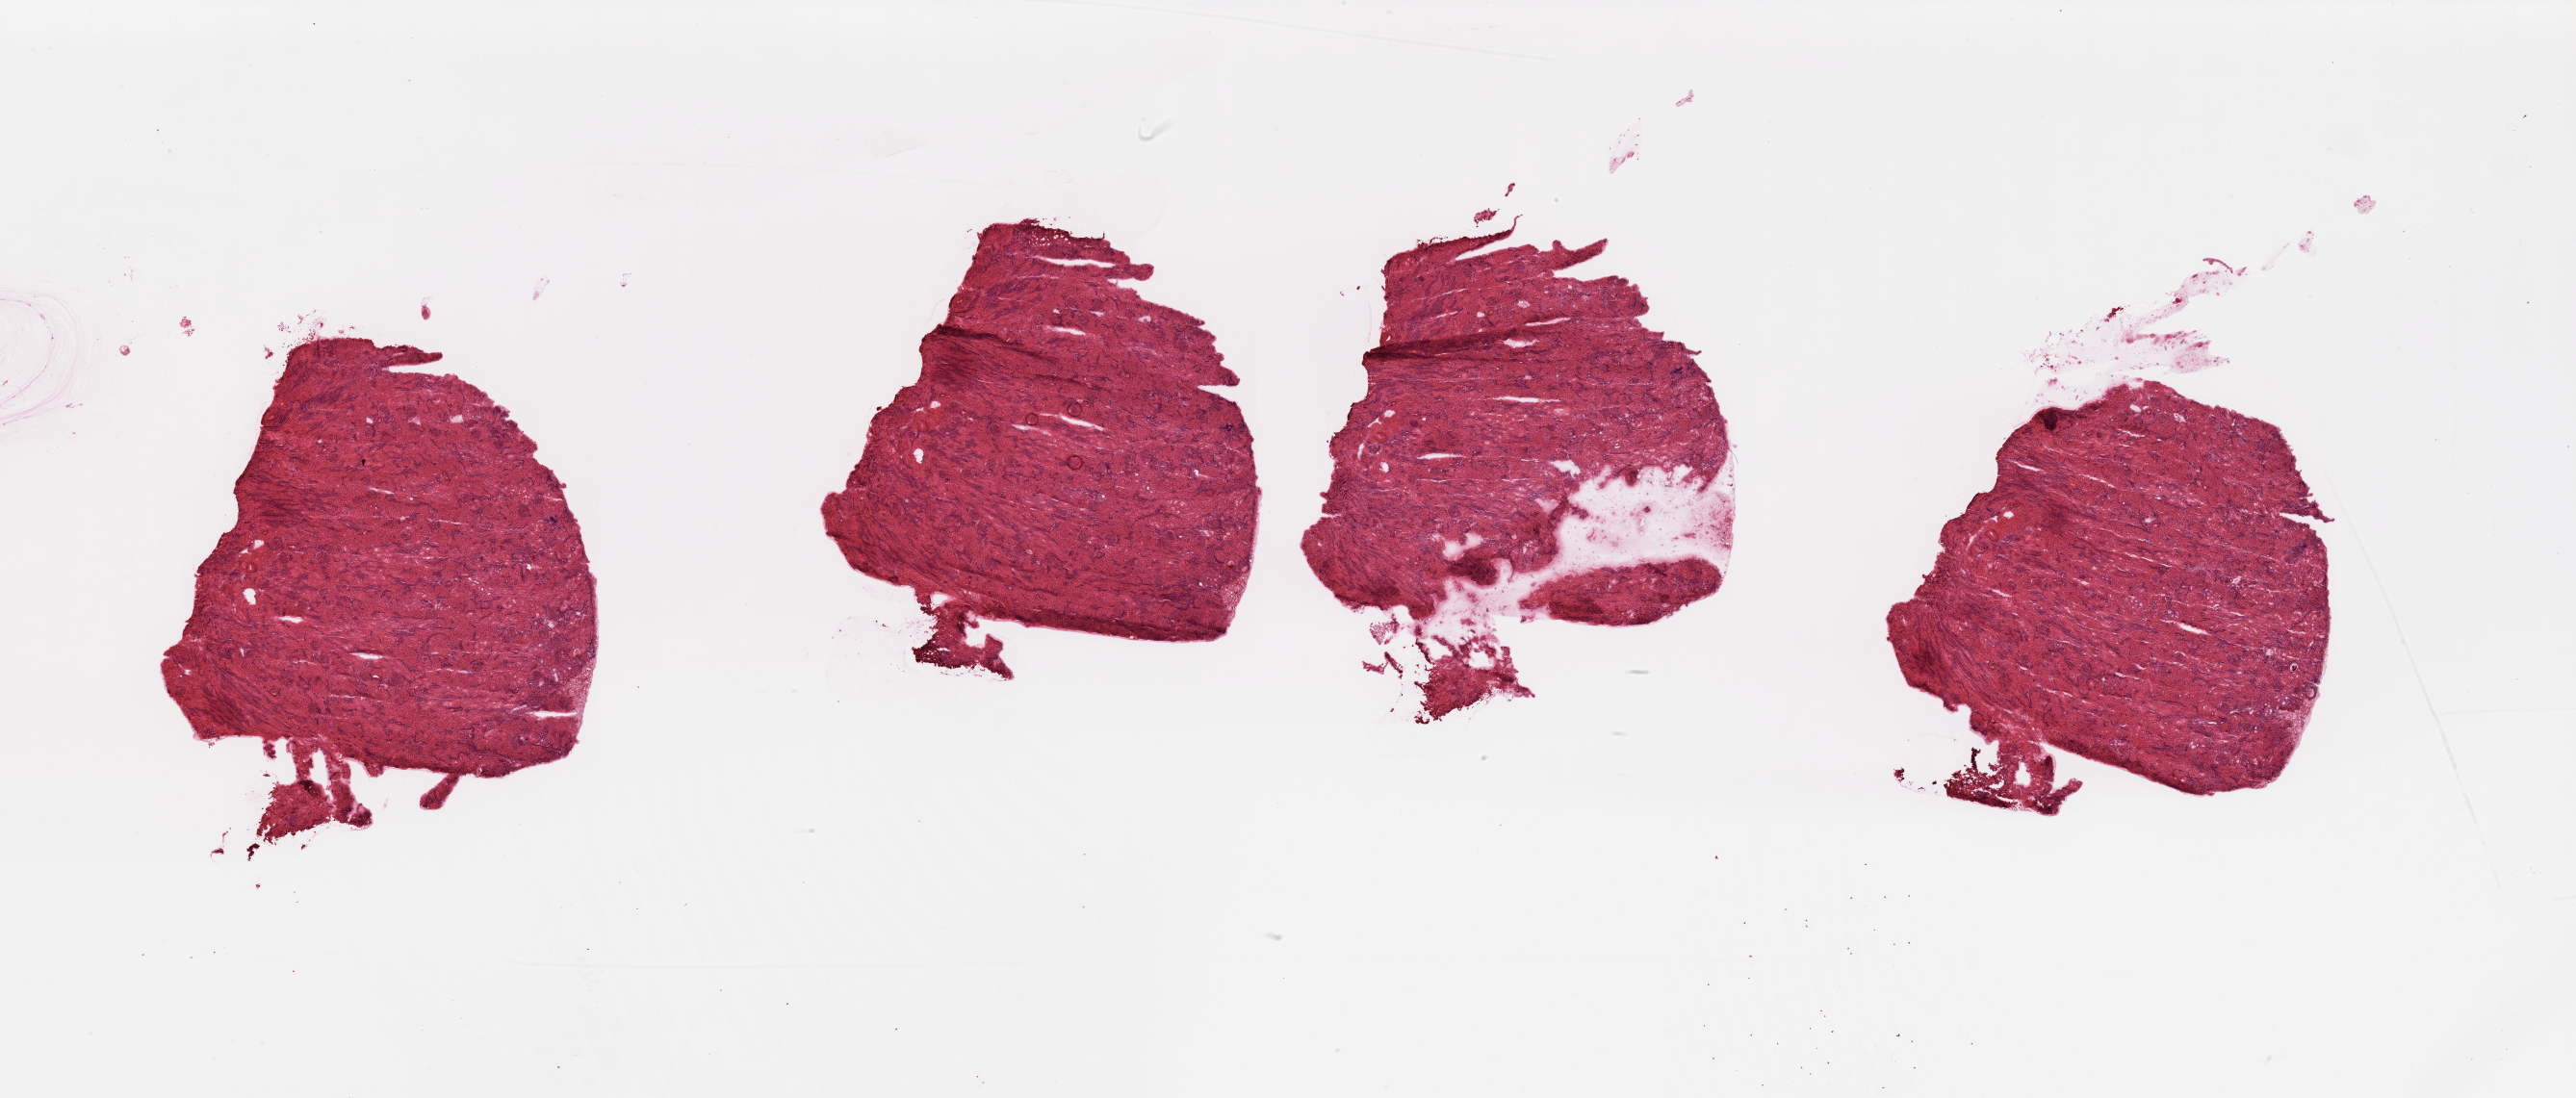
Digitized H&E tissue section (whole slide), low-resolution overview of the scanned area, about 42.3 x 18.0 mm (slide scanned at 20x), kidney, normal (non-tumour) tissue. Patient: male, age 54 years.
This section: normal (non-tumour) tissue from the same patient. Patient diagnosis: Renal cell carcinoma, NOS.